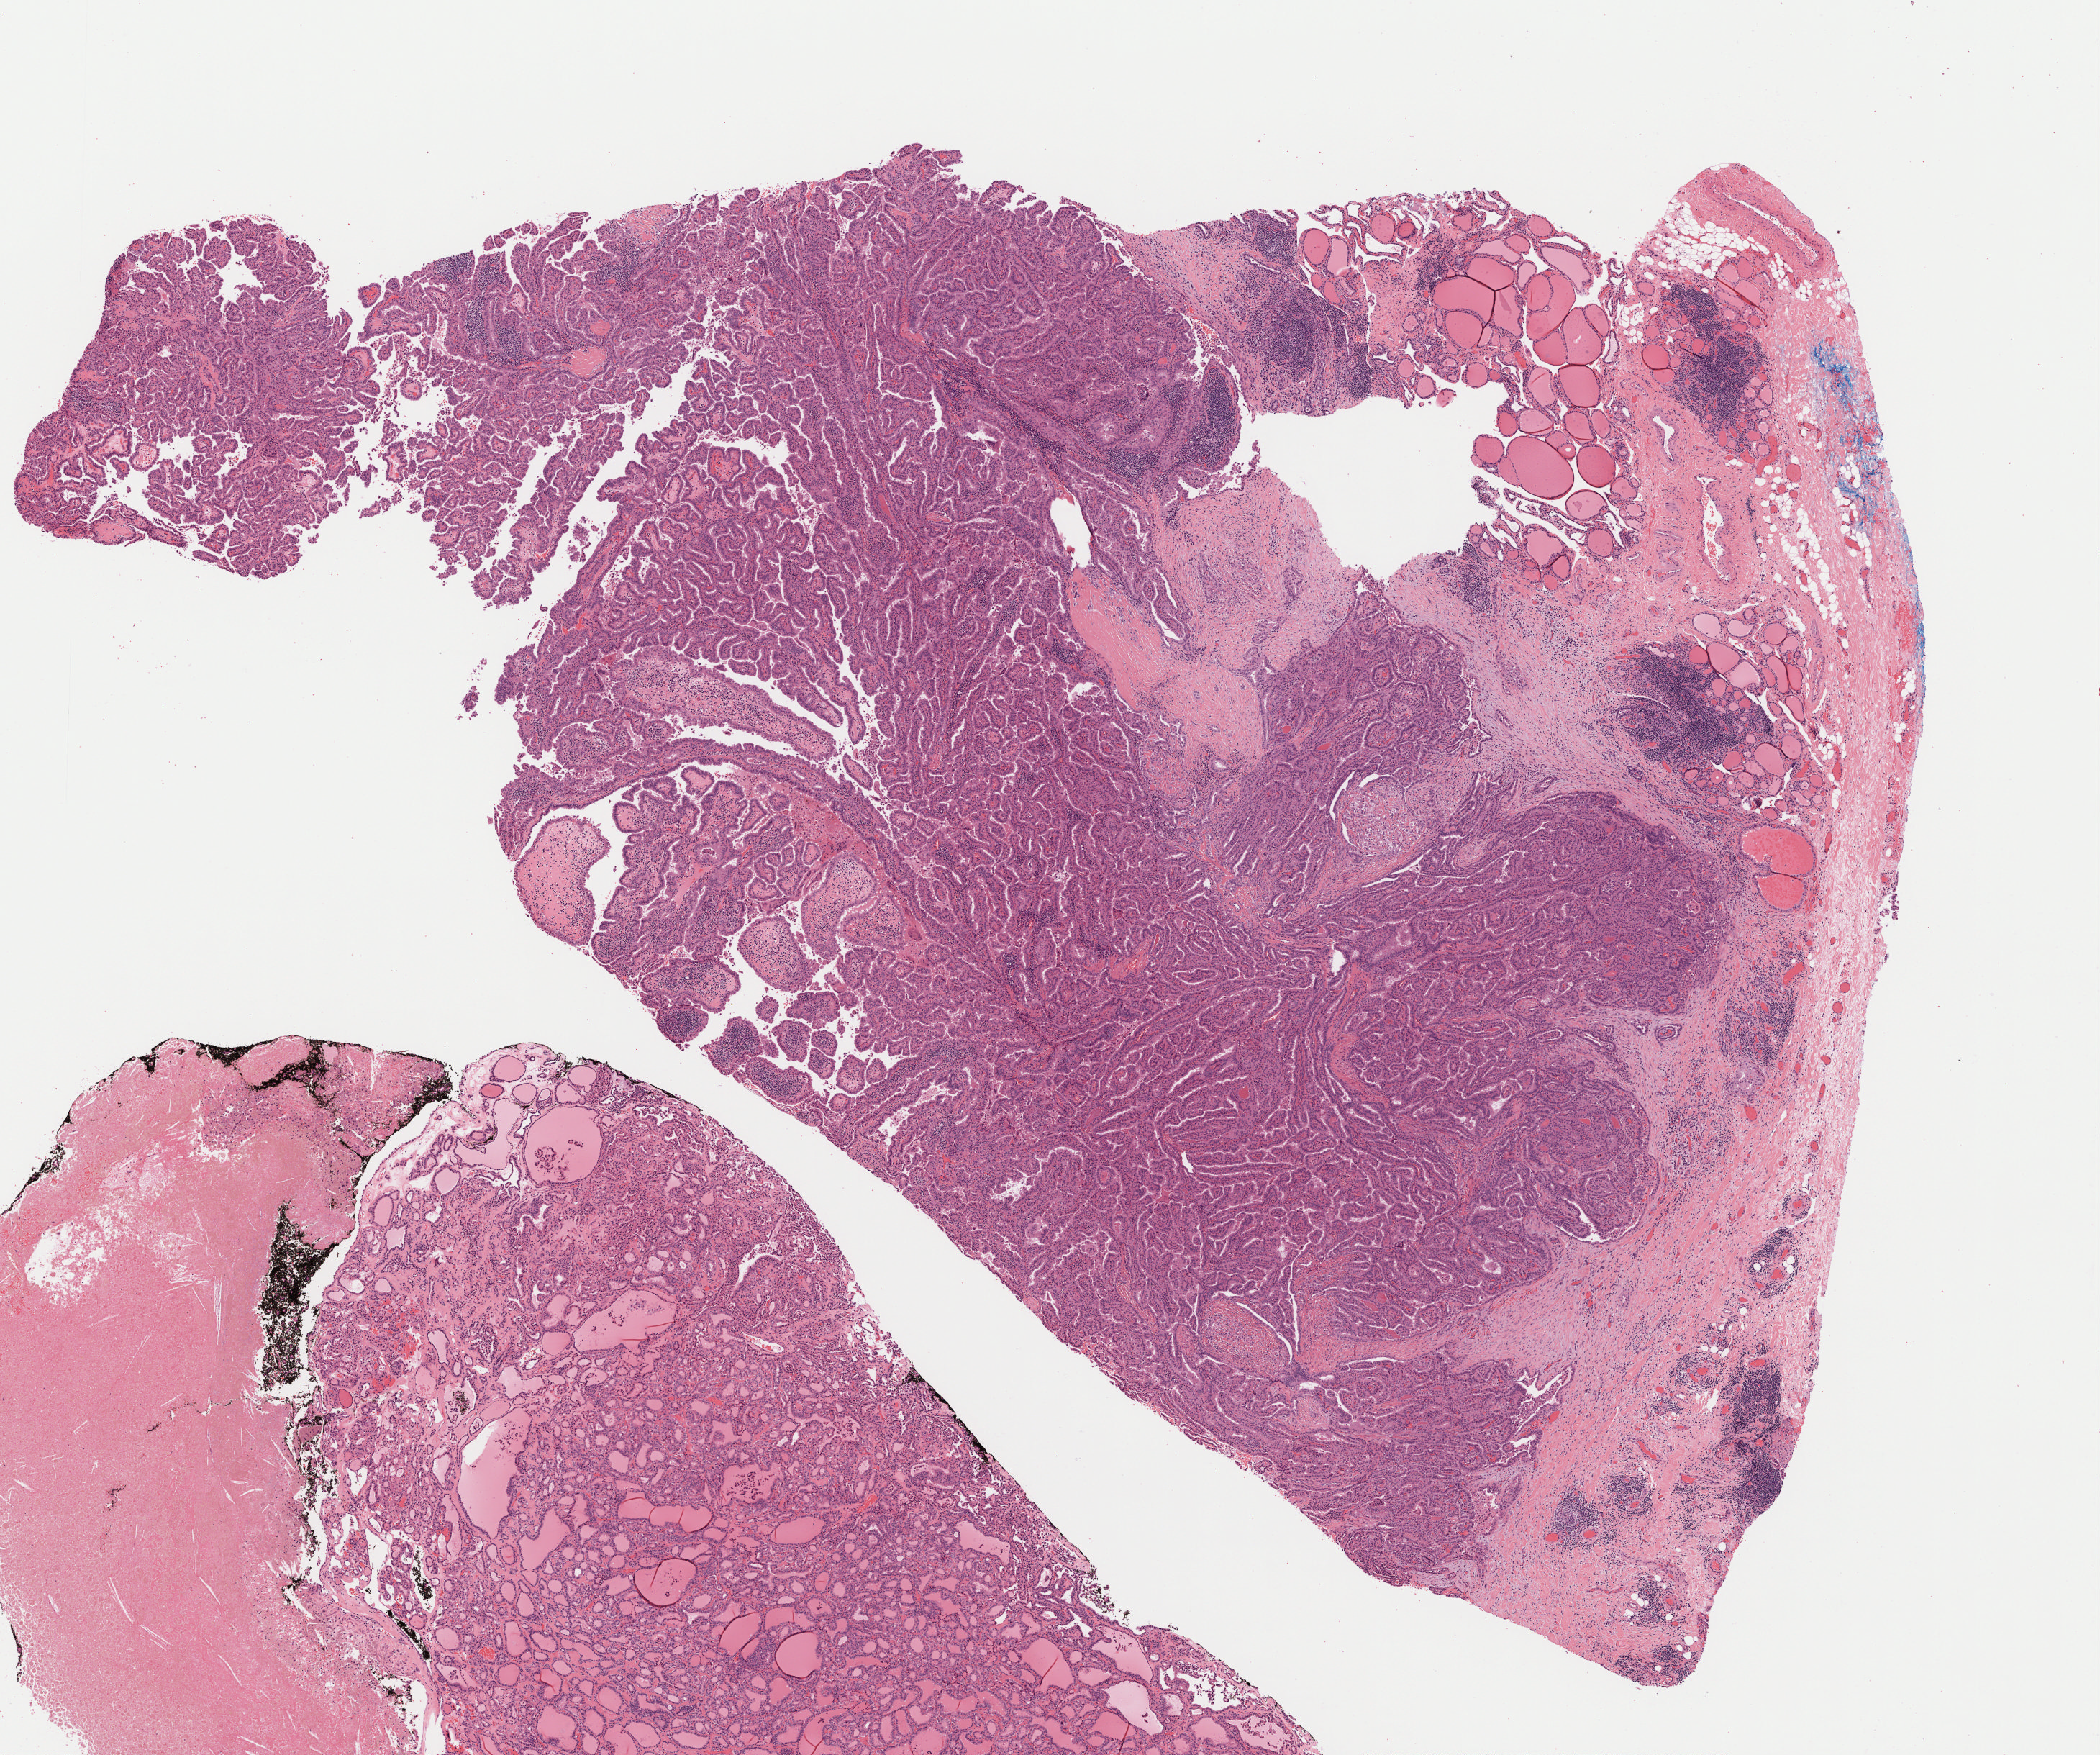
Whole-slide histology image, H&E — low-resolution overview of the scanned area, about 11.8 x 9.8 mm (acquisition: 40x scan), formalin-fixed paraffin-embedded (FFPE) diagnostic section, primary tumour sample from the thyroid. Female patient; age at initial diagnosis 42 years.
Pathologic diagnosis: Papillary carcinoma, follicular variant. AJCC pathologic stage: I (7th edition). TNM: T2 N1 MX.